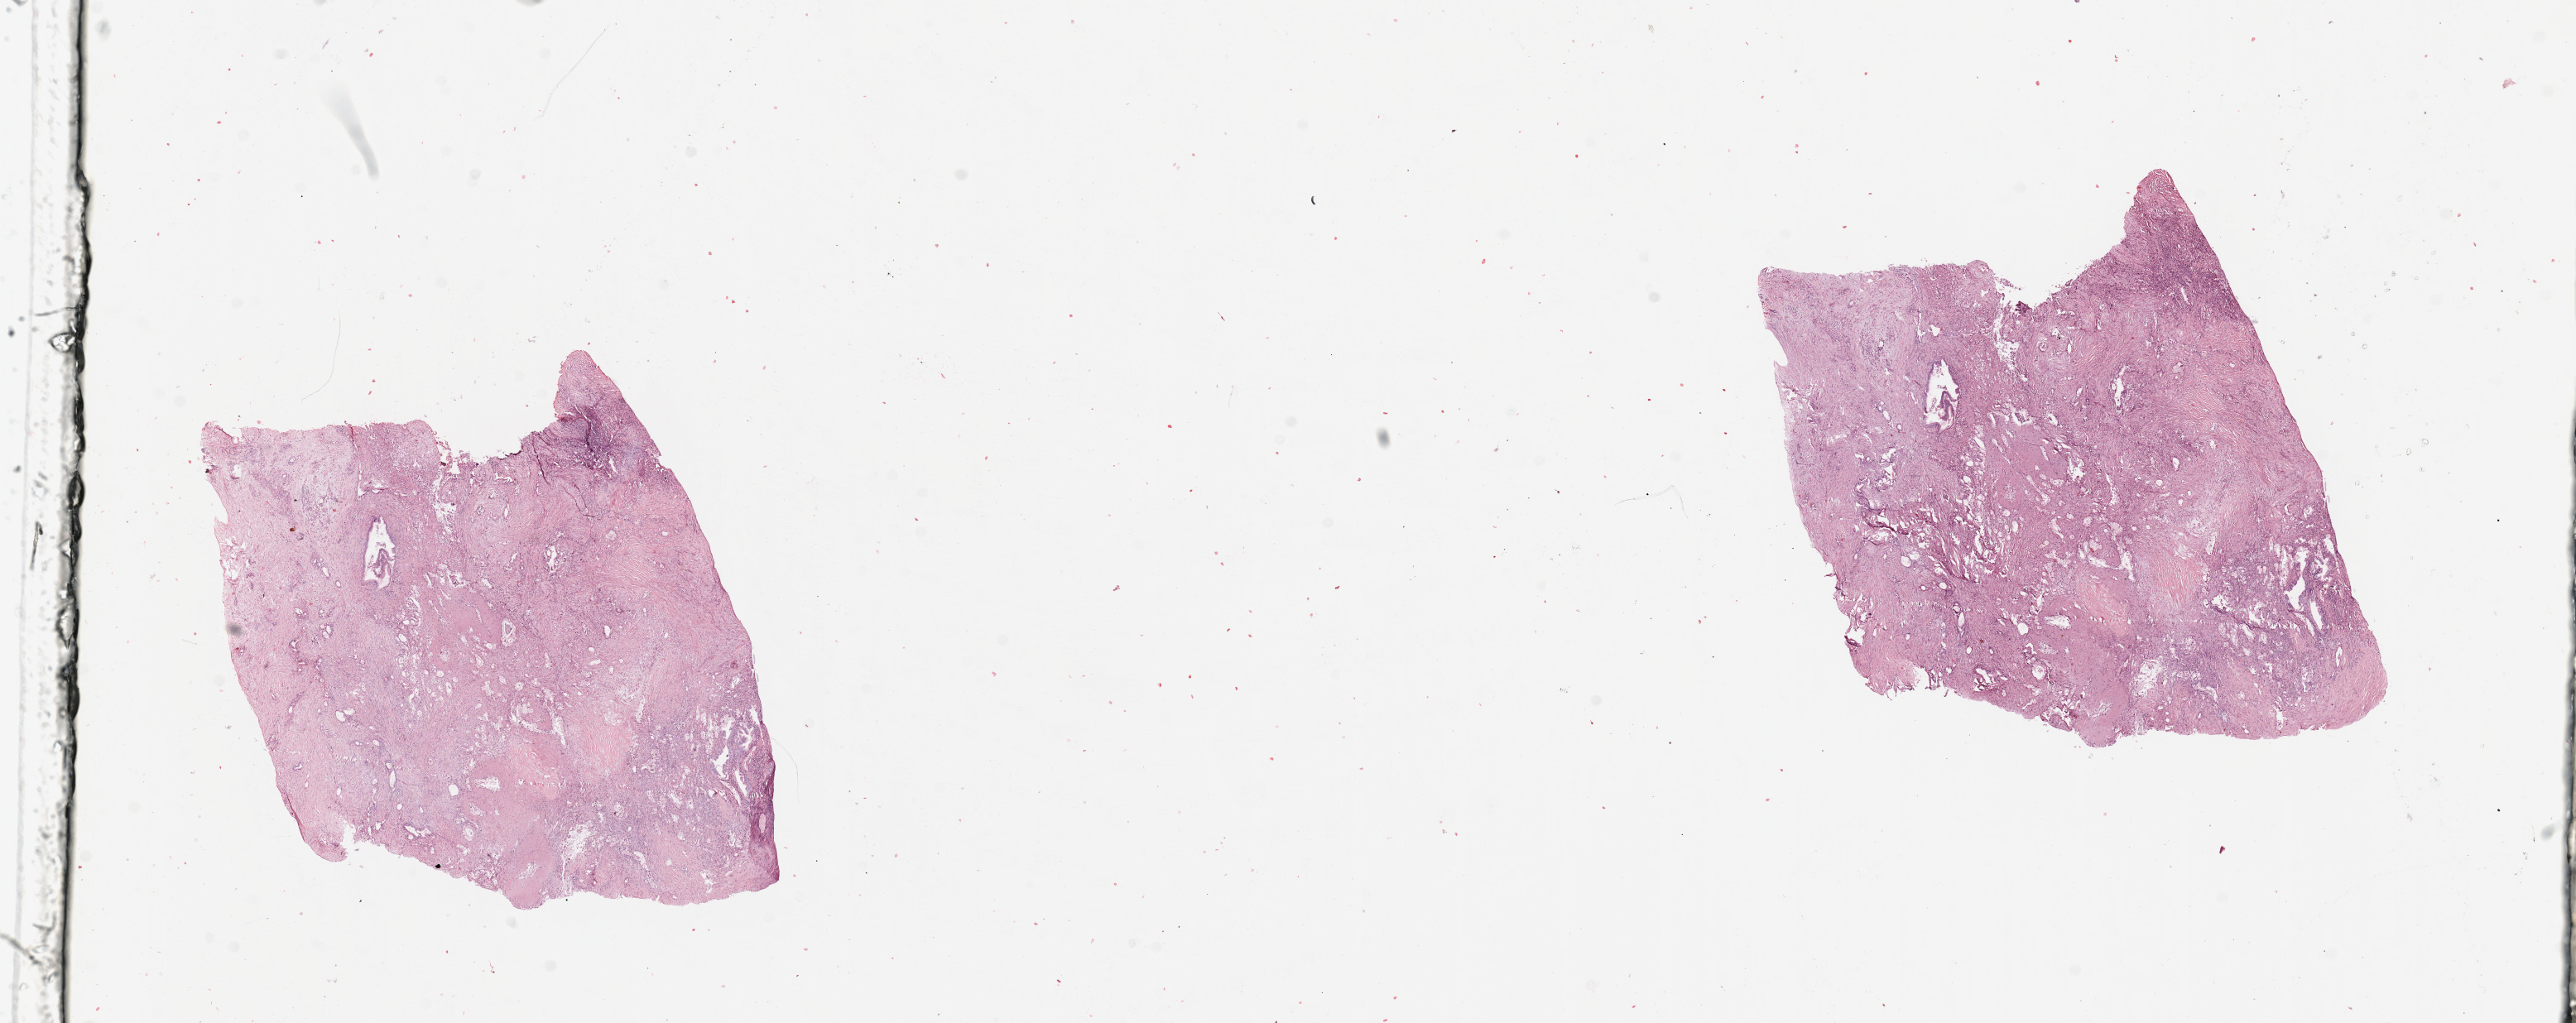
Whole-slide histology image, H&E-stained — whole scanned area (about 24.6 x 9.8 mm, from a 20x scan) shown as a low-resolution overview, pancreas, tissue type not recorded.
* patient diagnosis (cohort enrolment): ductal adenocarcinoma (pancreas)